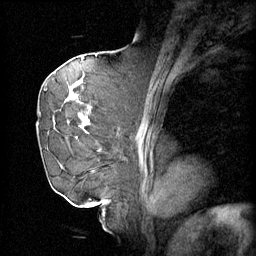
Breast MRI (dynamic contrast-enhanced), one sagittal slice; slice 33 of 60 in the series (ordered by position); 4 images stored at this slice position (order not interpretable as contrast timing); 1.5 T; TE 4.2 ms, TR 11 ms; 2 mm slice thickness; 256 × 256 image matrix, field of view 220 × 220 mm. Patient: female, 72 years.
Annotated regions visible in this slice (semi-automatic segmentation, software-assisted and operator-edited):
- analysis volume of interest (the breast-tissue region the enhancement analysis was run in; not a lesion): bounding box [x1, y1, x2, y2] px = [44, 68, 108, 163]
- tumour enhancement mask (voxels above the 70 % enhancement threshold inside the analysis volume of interest): [52, 74, 99, 135]